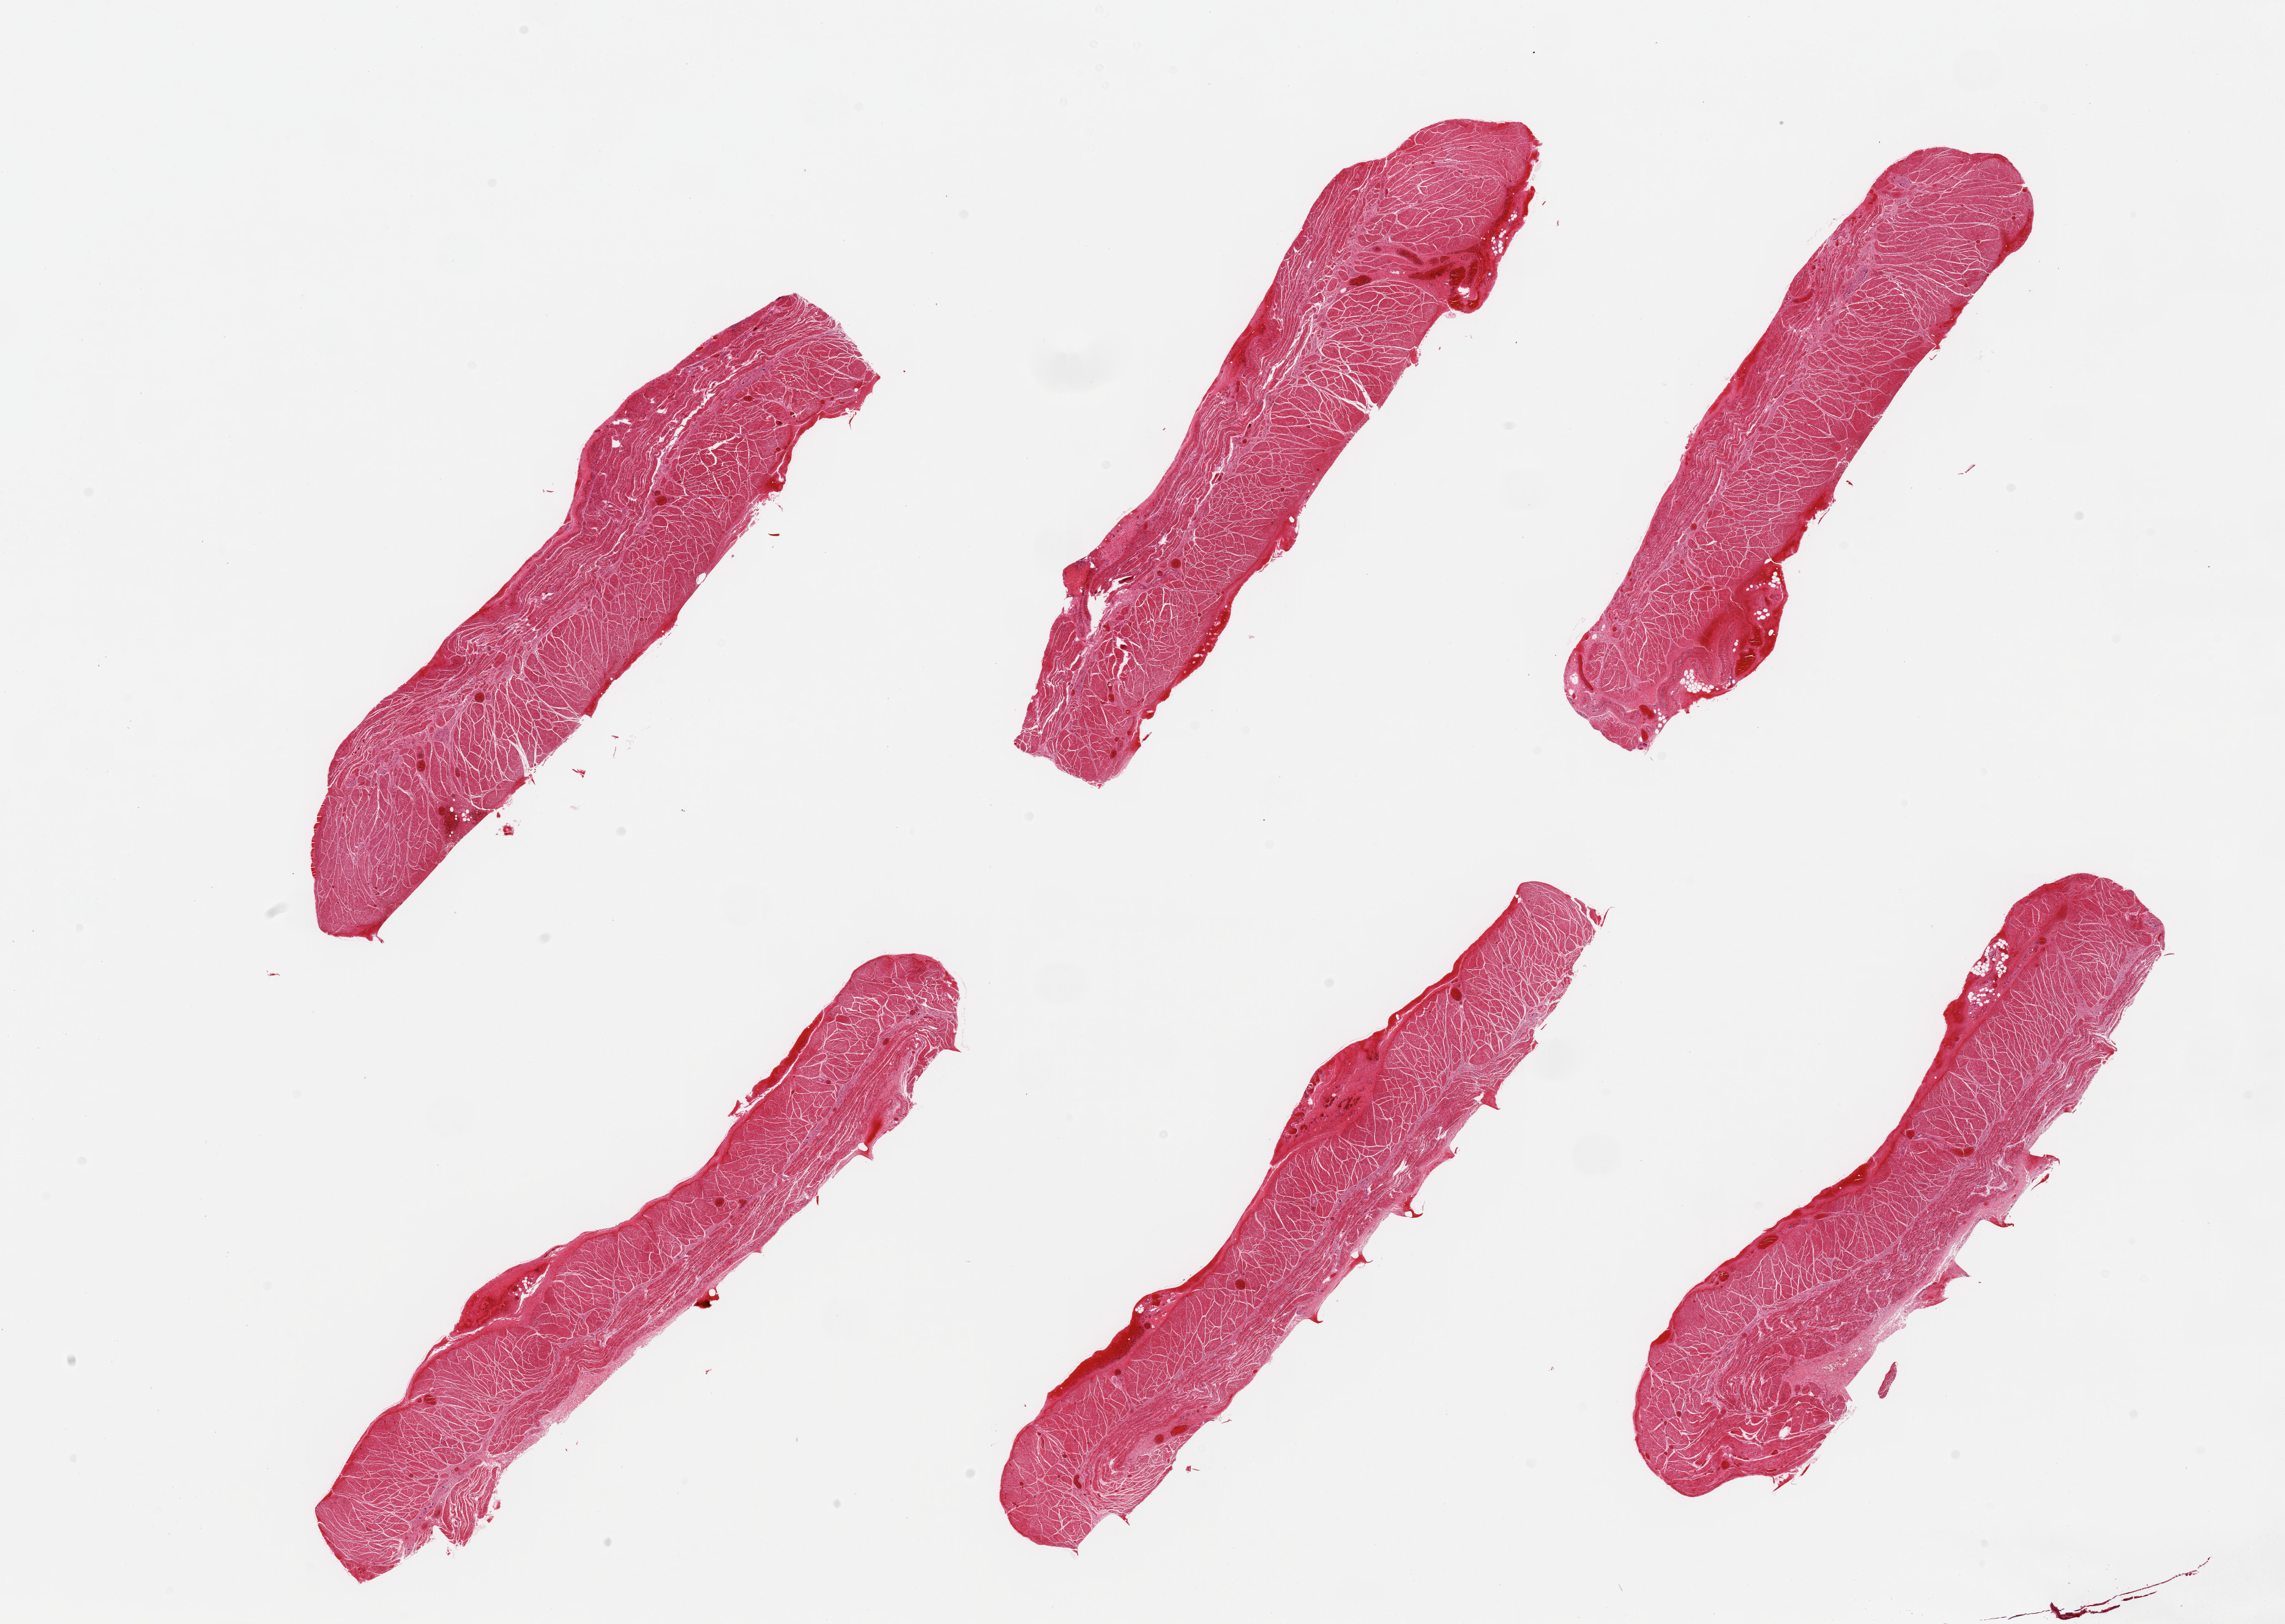
Whole-slide image, haematoxylin and eosin stain, brightfield — shown as a low-resolution overview of the whole scanned area (about 29.5 x 21.0 mm, acquisition: 20x scan); PAXgene-fixed paraffin-embedded (PFPE) section; target tissue: esophageal muscle; tissue donor sample. Donor: male.
Reviewer comment on this tissue sample: 6 pieces; well trimmed.